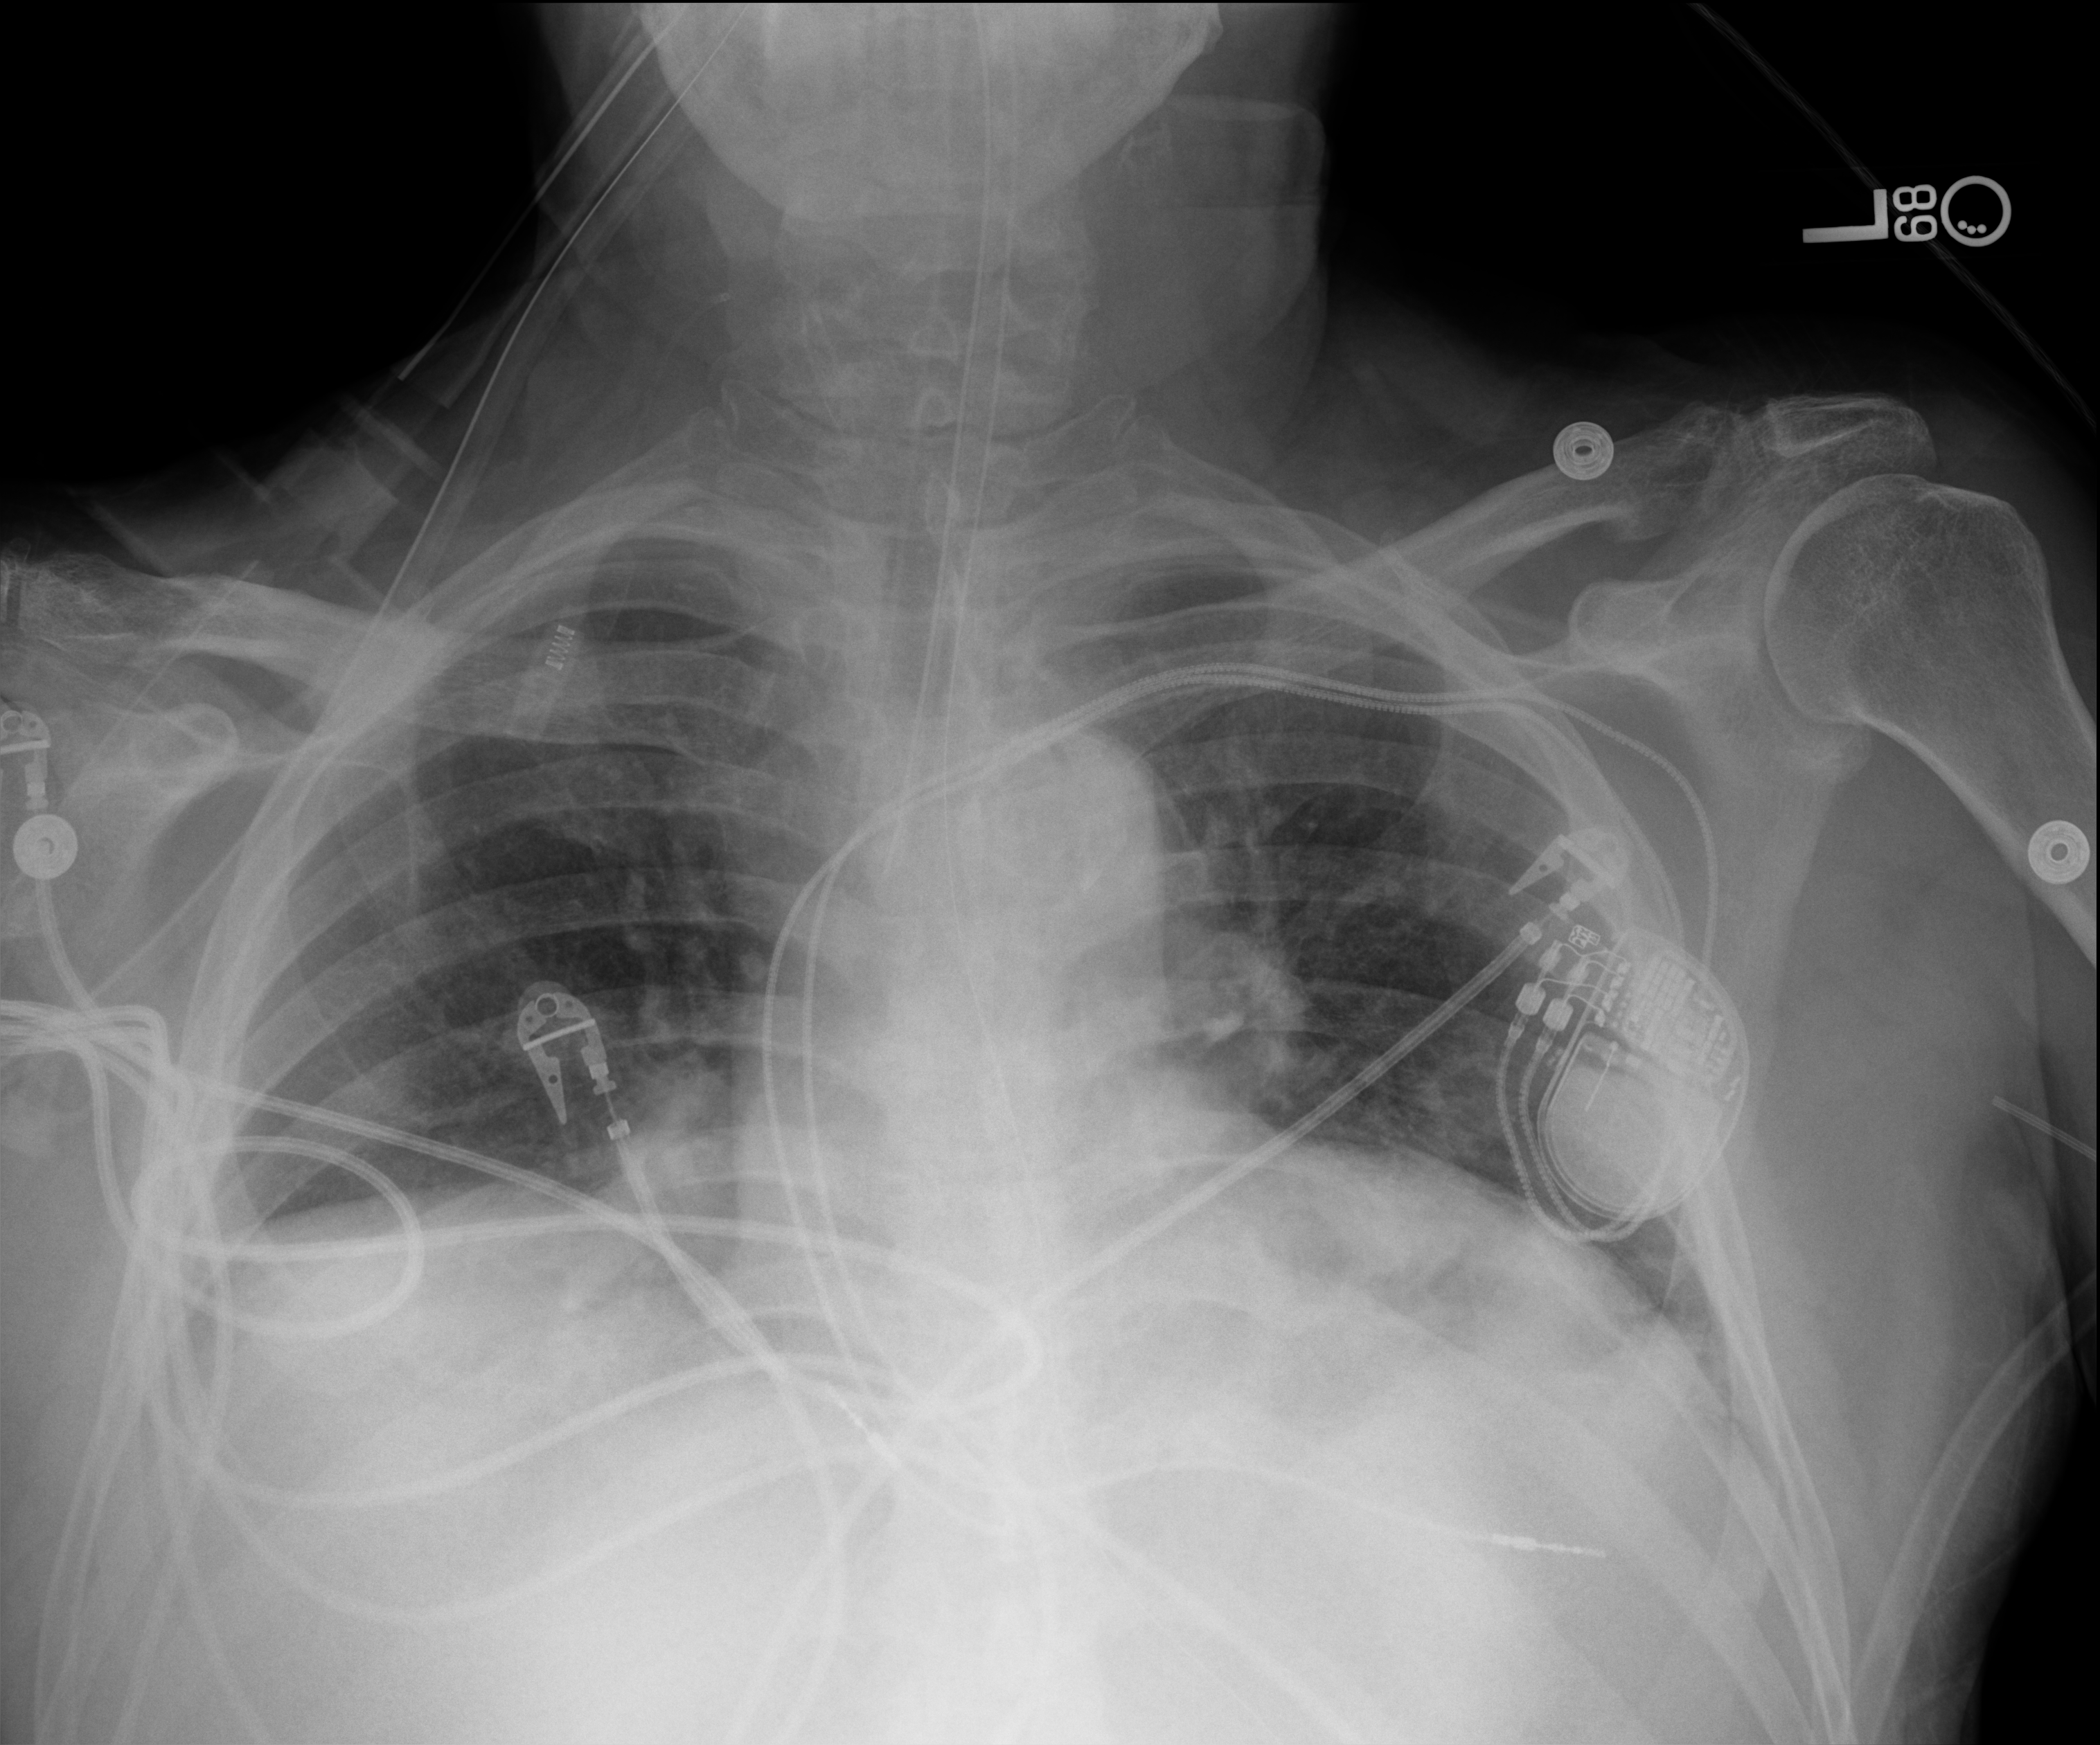
Chest X-ray (portable); anteroposterior (AP) projection. Male patient hospitalised with COVID-19, age 60–74 years.
Hospital-stay facts (about this admission, not read from this image; timing relative to this image not recorded):
- admitted to intensive care during this hospital stay: yes
- mechanically ventilated during this hospital stay: yes